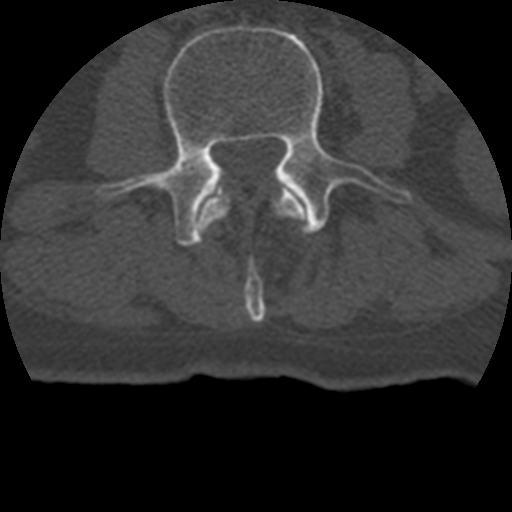
CT including the spine, one axial slice; position 97 of 399 along the scan axis; reconstruction kernel STANDARD; 120 kVp; bone window (W 1800 / L 400 HU); 512 × 512 image matrix. Patient age 69 years. From the clinical record (not read from this slice): primary cancer: prostate.
Outlined on this slice (semi-automatic segmentation, software-assisted and operator-edited):
- L2 vertebra: bounding box (x1, y1, x2, y2) in pixels: (199, 190, 306, 322)
- L3 vertebra: (95, 25, 411, 246)